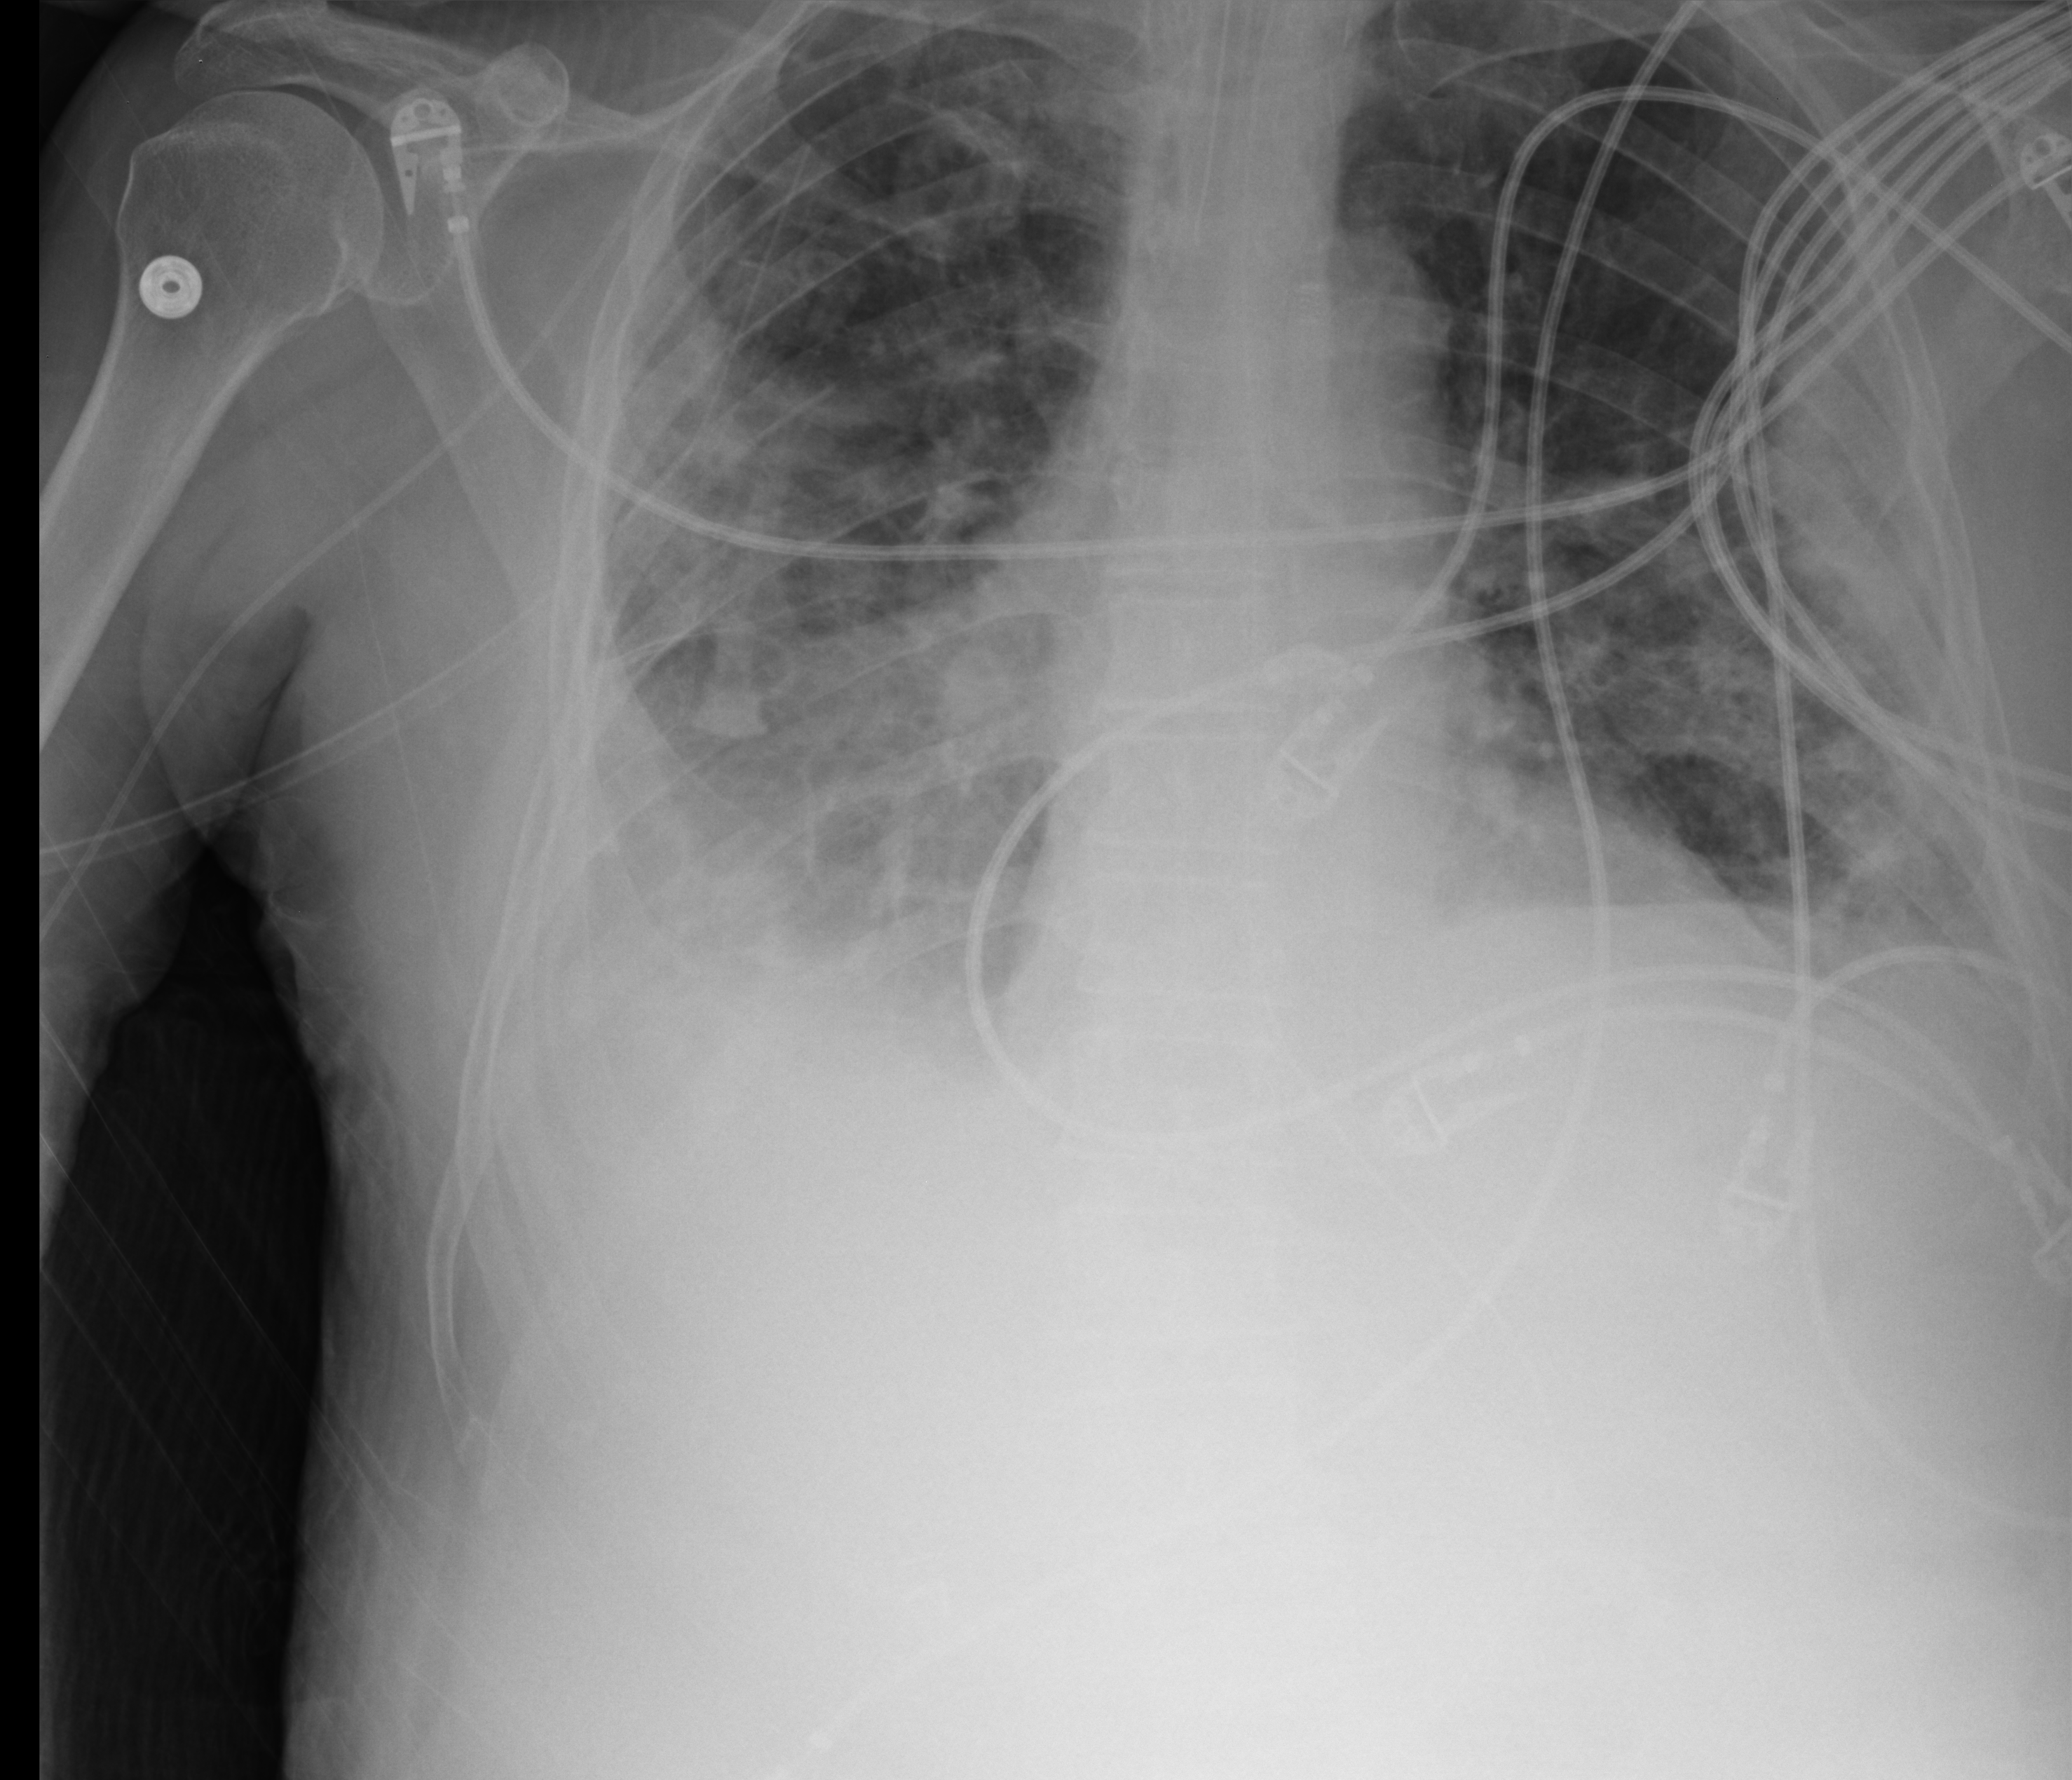
Portable chest radiograph; anteroposterior (AP) projection. Male patient hospitalised with COVID-19, age 75–90 years.
Admission-level facts for this patient (not findings on this image; timing relative to this image not recorded):
- admitted to intensive care during this hospital stay: yes
- other chronic lung disease (admission record): yes
- hypertension (admission record): no